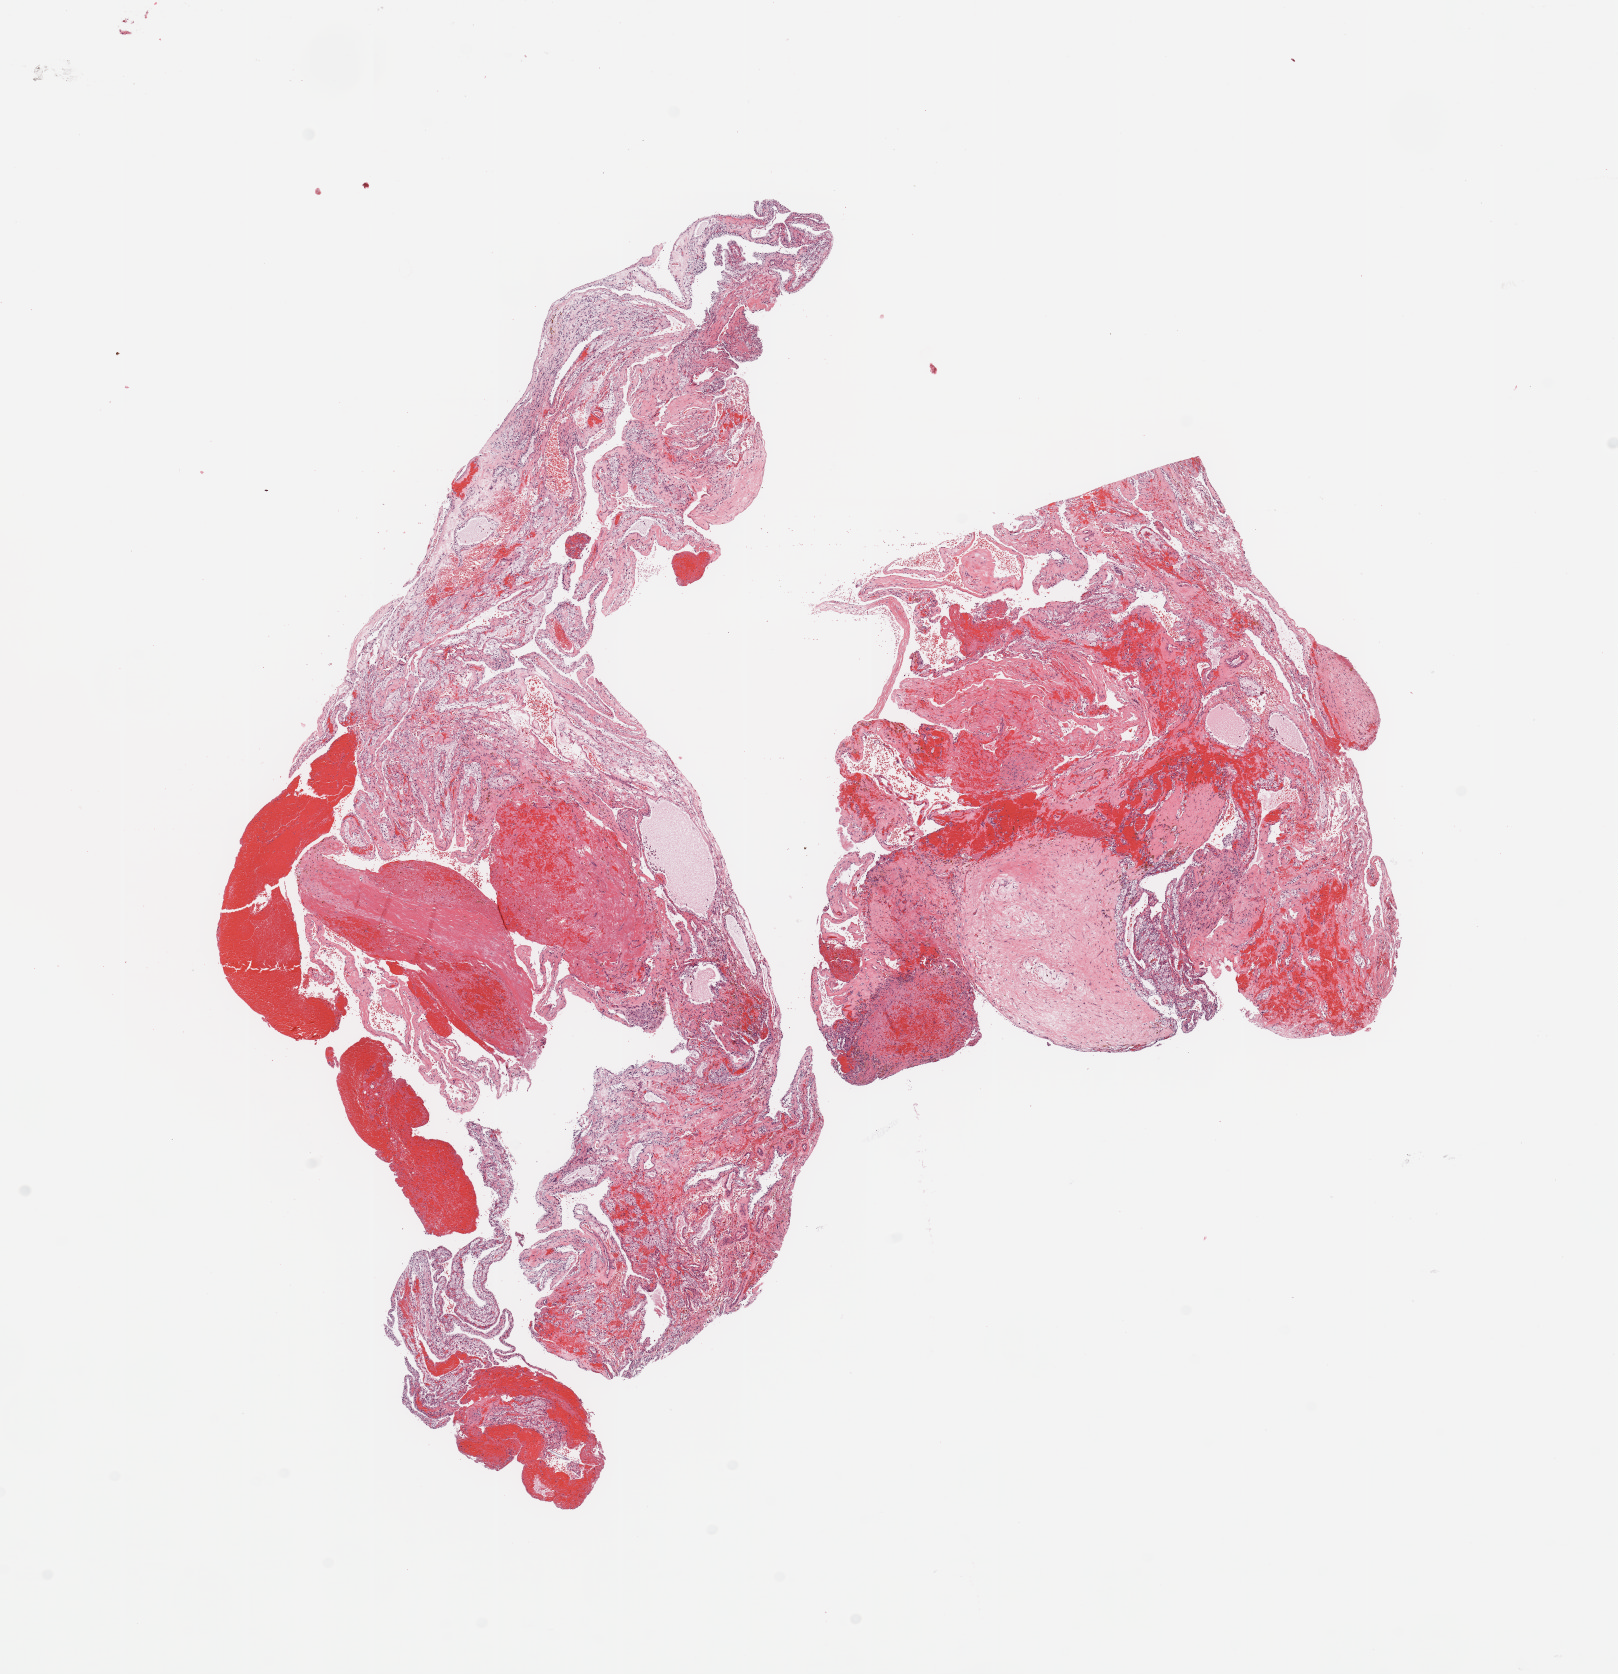
Whole-slide histology image, Hematoxylin and eosin (H&E) stained — whole scanned area (about 12.8 x 13.2 mm, from a 20x scan) shown as a low-resolution overview; tumour tissue sample, sampled site: kidney. Female, 67 y/o. Histologic grade: G3 (poorly differentiated). Slide review estimates, as recorded: tumour nuclei 80%, necrosis 5%.
AJCC pathologic stage: I. Primary tumour site (as recorded): lower pole. Histologic diagnosis: Renal cell carcinoma, NOS.